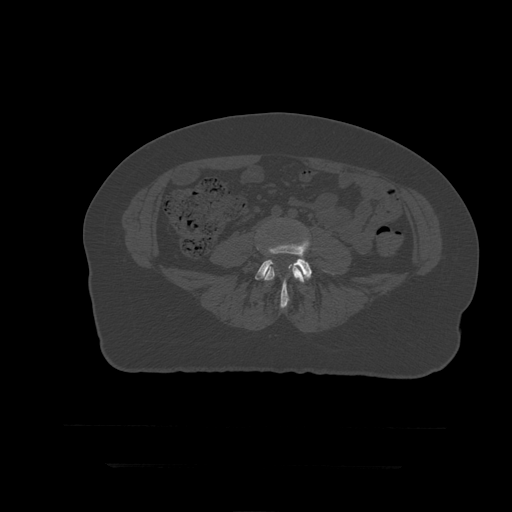
CT including the spine, one axial slice. Position 83 of 399 along the scan axis. 120 kVp. Bone window (W 1800 / L 400 HU). 1.25 mm slice thickness. 512 × 512 image matrix. Patient age 41 years. From the clinical record (not read from this slice): primary cancer: breast.
Structures marked on this image (semi-automatic segmentation, software-assisted and operator-edited):
- L4 vertebra: bounding box [x1, y1, x2, y2] px = [257, 218, 305, 299]
- L5 vertebra: [255, 240, 334, 309]